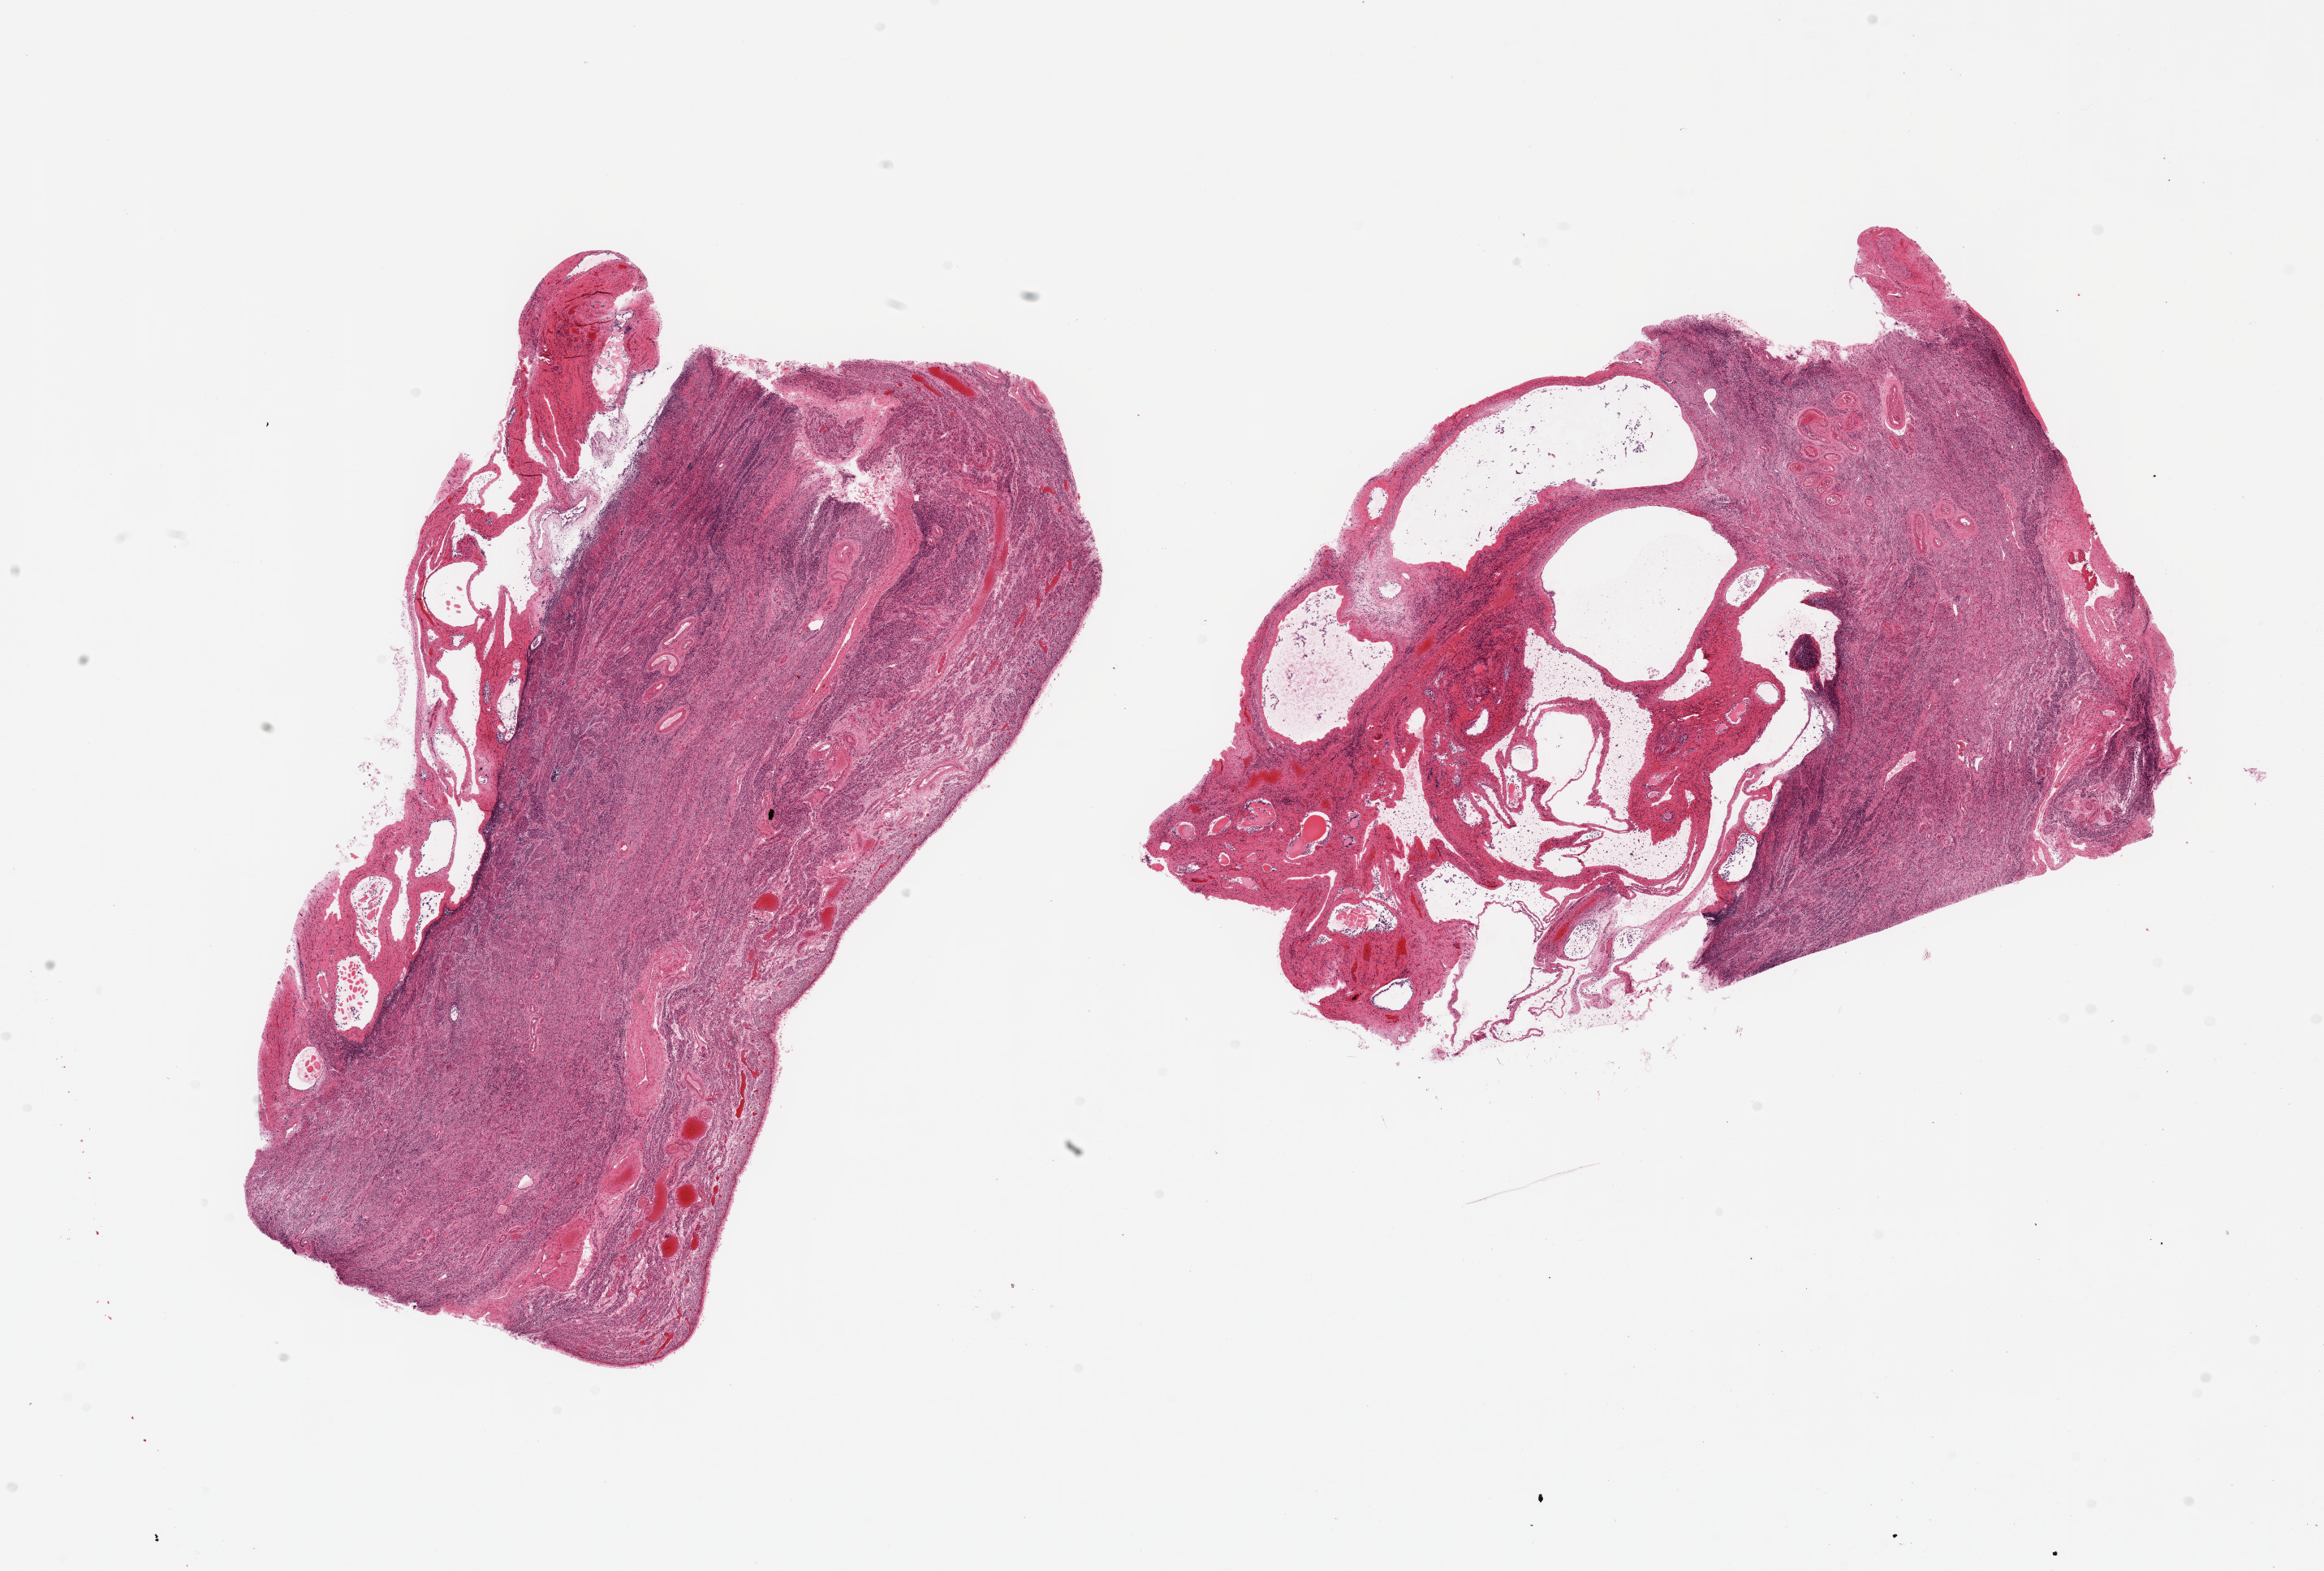
H&E whole-slide image, a low-resolution overview of the entire scanned area, about 22.6 x 15.3 mm. PAXgene-fixed, paraffin-embedded tissue. Sampled site (target tissue): uterus. Donor tissue sample. Donor sex: female.
Pathologist's review note for this sample: 2 pieces, mainly myoetrium; autolyzed 6x6mm cystic endometrial polyp.